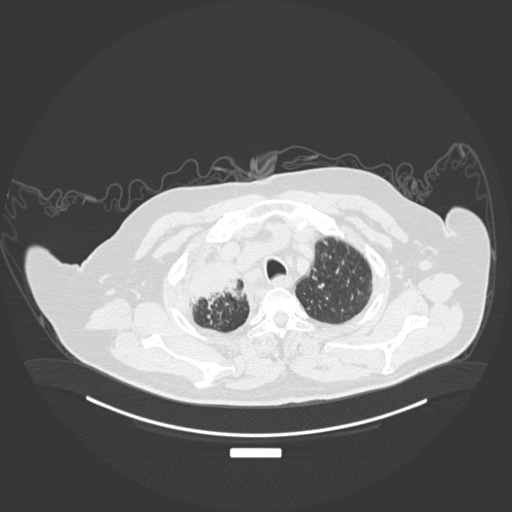
Chest CT, one axial slice. Position 164 of 201 along the scan axis. Reconstruction kernel B30f. Lung window (W 1500 / L -600 HU). 1 mm slice thickness. 512 × 512 image matrix, field of view 500 × 500 mm. Patient: male, 69 years. Case-level facts recorded for this patient, not image findings: clinical TNM (as recorded): T4 N3 M1.
Annotated regions visible in this slice (rectangle marked by the reading radiologist):
- lung tumour (recorded histology: adenocarcinoma): box from (x=190, y=254) to (x=245, y=306) px